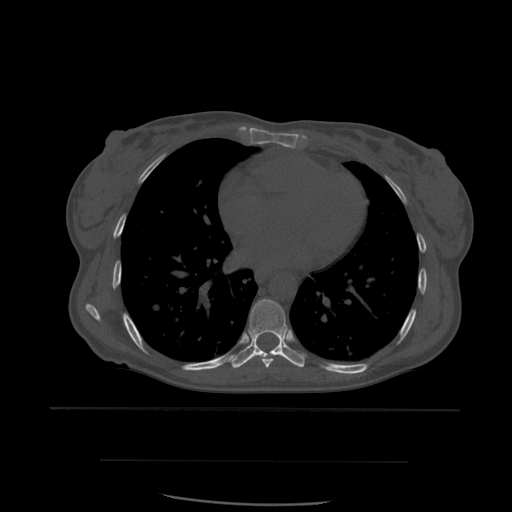
CT including the spine, one axial slice; position 361 of 574 along the scan axis; bone window (W 1800 / L 400 HU); 1.25 mm slice thickness; 512 × 512 image matrix, field of view 392 × 392 mm. Patient age 48 years. From the clinical record (not read from this slice): primary cancer: lung.
Outlined on this slice (semi-automatically segmented with operator editing):
- T6 vertebra: bounding box [x1, y1, x2, y2] px = [249, 332, 255, 339]
- T7 vertebra: [261, 357, 274, 368]
- T8 vertebra: [231, 299, 305, 369]